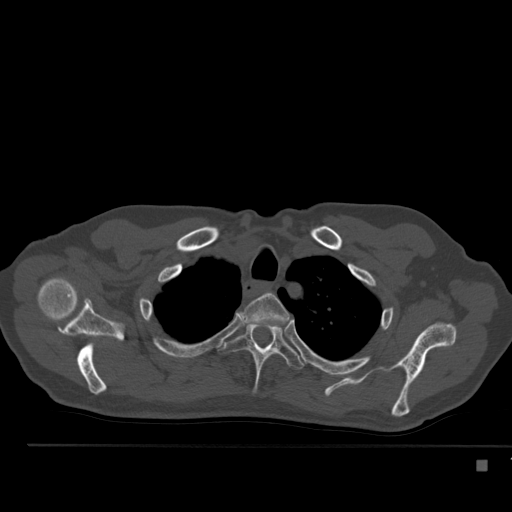
CT including the spine, one axial slice. Slice 402 of 517 in the series (ordered by position). Reconstruction kernel Br40s. 120 kVp. Bone window (W 1800 / L 400 HU). 1.5 mm slice thickness. 512 × 512 image matrix, field of view 408 × 408 mm. Male patient, age 70 years. Case-level facts recorded for this patient, not image findings: primary cancer: renal; vertebrae with lytic lesions (as recorded): T4, T6, T10, T12, L3, L4, L5.
Outlined on this slice (semi-automatically segmented with operator editing):
- T2 vertebra: bounding box [x1, y1, x2, y2] px = [242, 293, 290, 325]
- T3 vertebra: [218, 323, 304, 394]